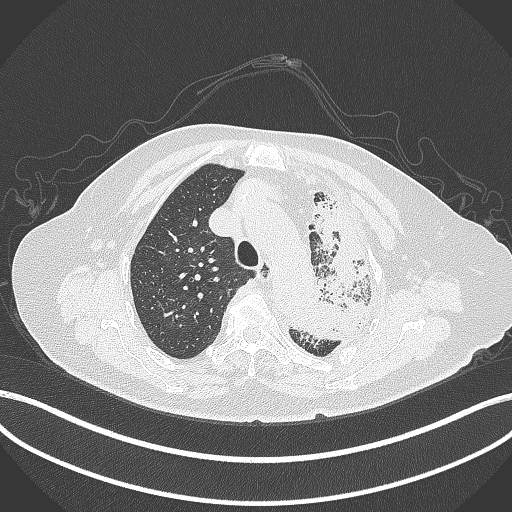
Chest CT, one axial slice. Slice 297 of 399 in the series (ordered by position). Reconstruction kernel B70f. Lung window (W 1500 / L -600 HU). 512 × 512 image matrix. Patient: female, 75 years. From the clinical record (not read from this slice): clinical TNM (as recorded): T3 N3 M1.
Annotated regions visible in this slice (rectangle marked by the reading radiologist):
- lung tumour (recorded histology: adenocarcinoma): bounding box <295,188,380,344> (left, top, right, bottom; pixels)